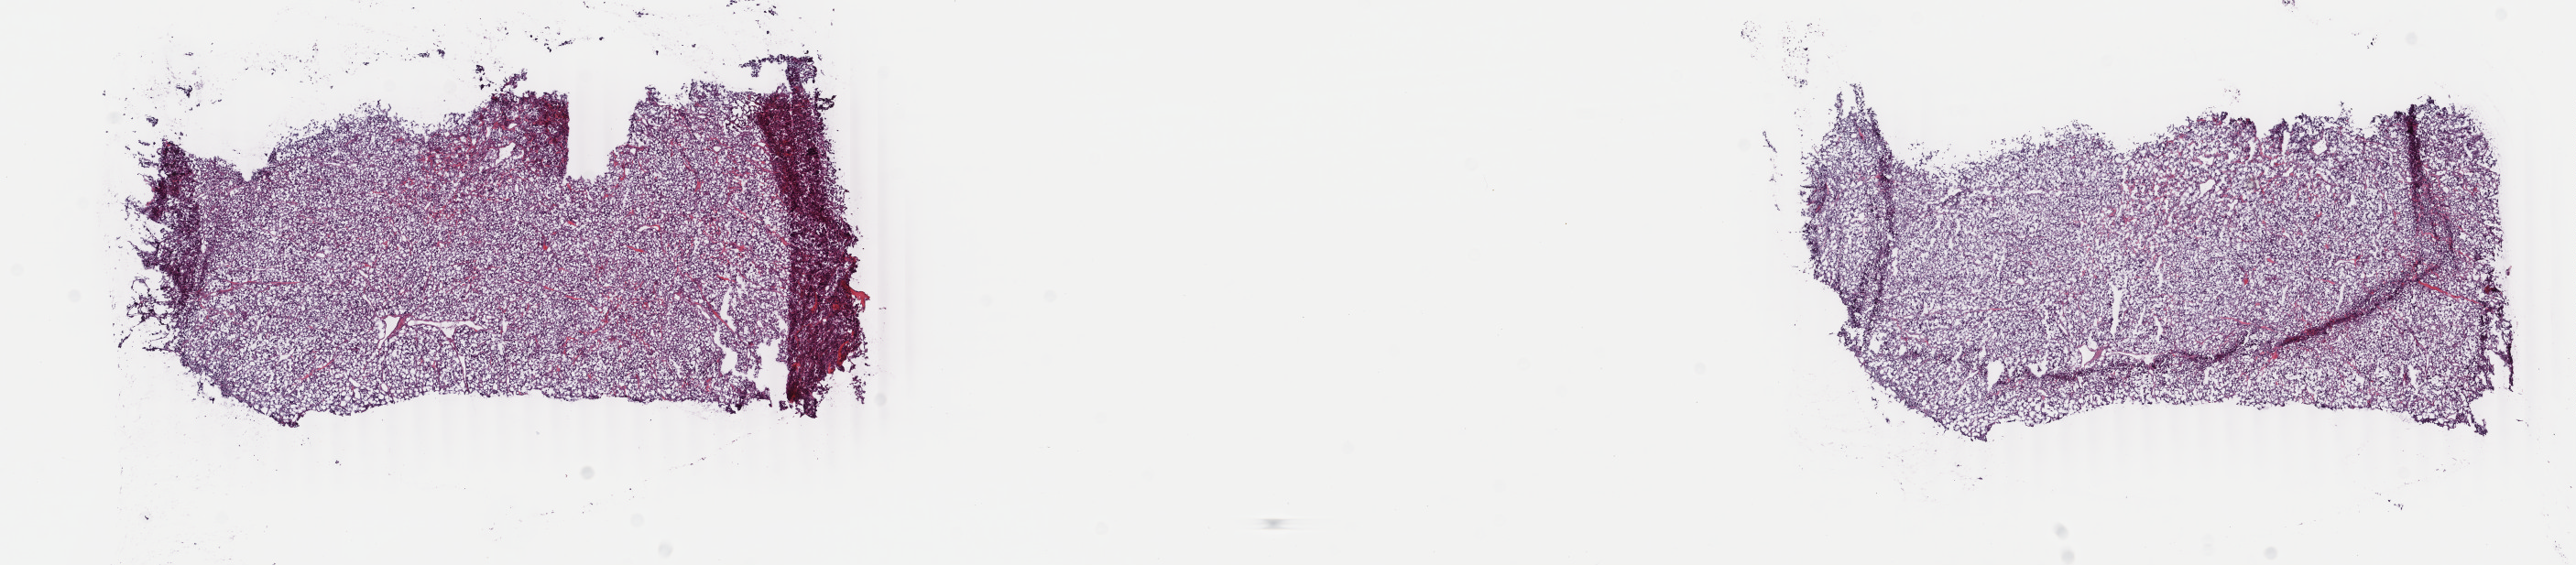
H&E-stained whole-slide image — low-resolution overview of the scanned area, about 22.4 x 4.9 mm (slide scanned at 40x). Frozen section. Sample: primary tumour, adrenal gland. Patient: female, age at initial diagnosis 51 years. Slide review estimates, as recorded: tumour cells 95%, tumour nuclei 100%.
Histologic diagnosis: Papillary adenocarcinoma, NOS (thyroid gland).